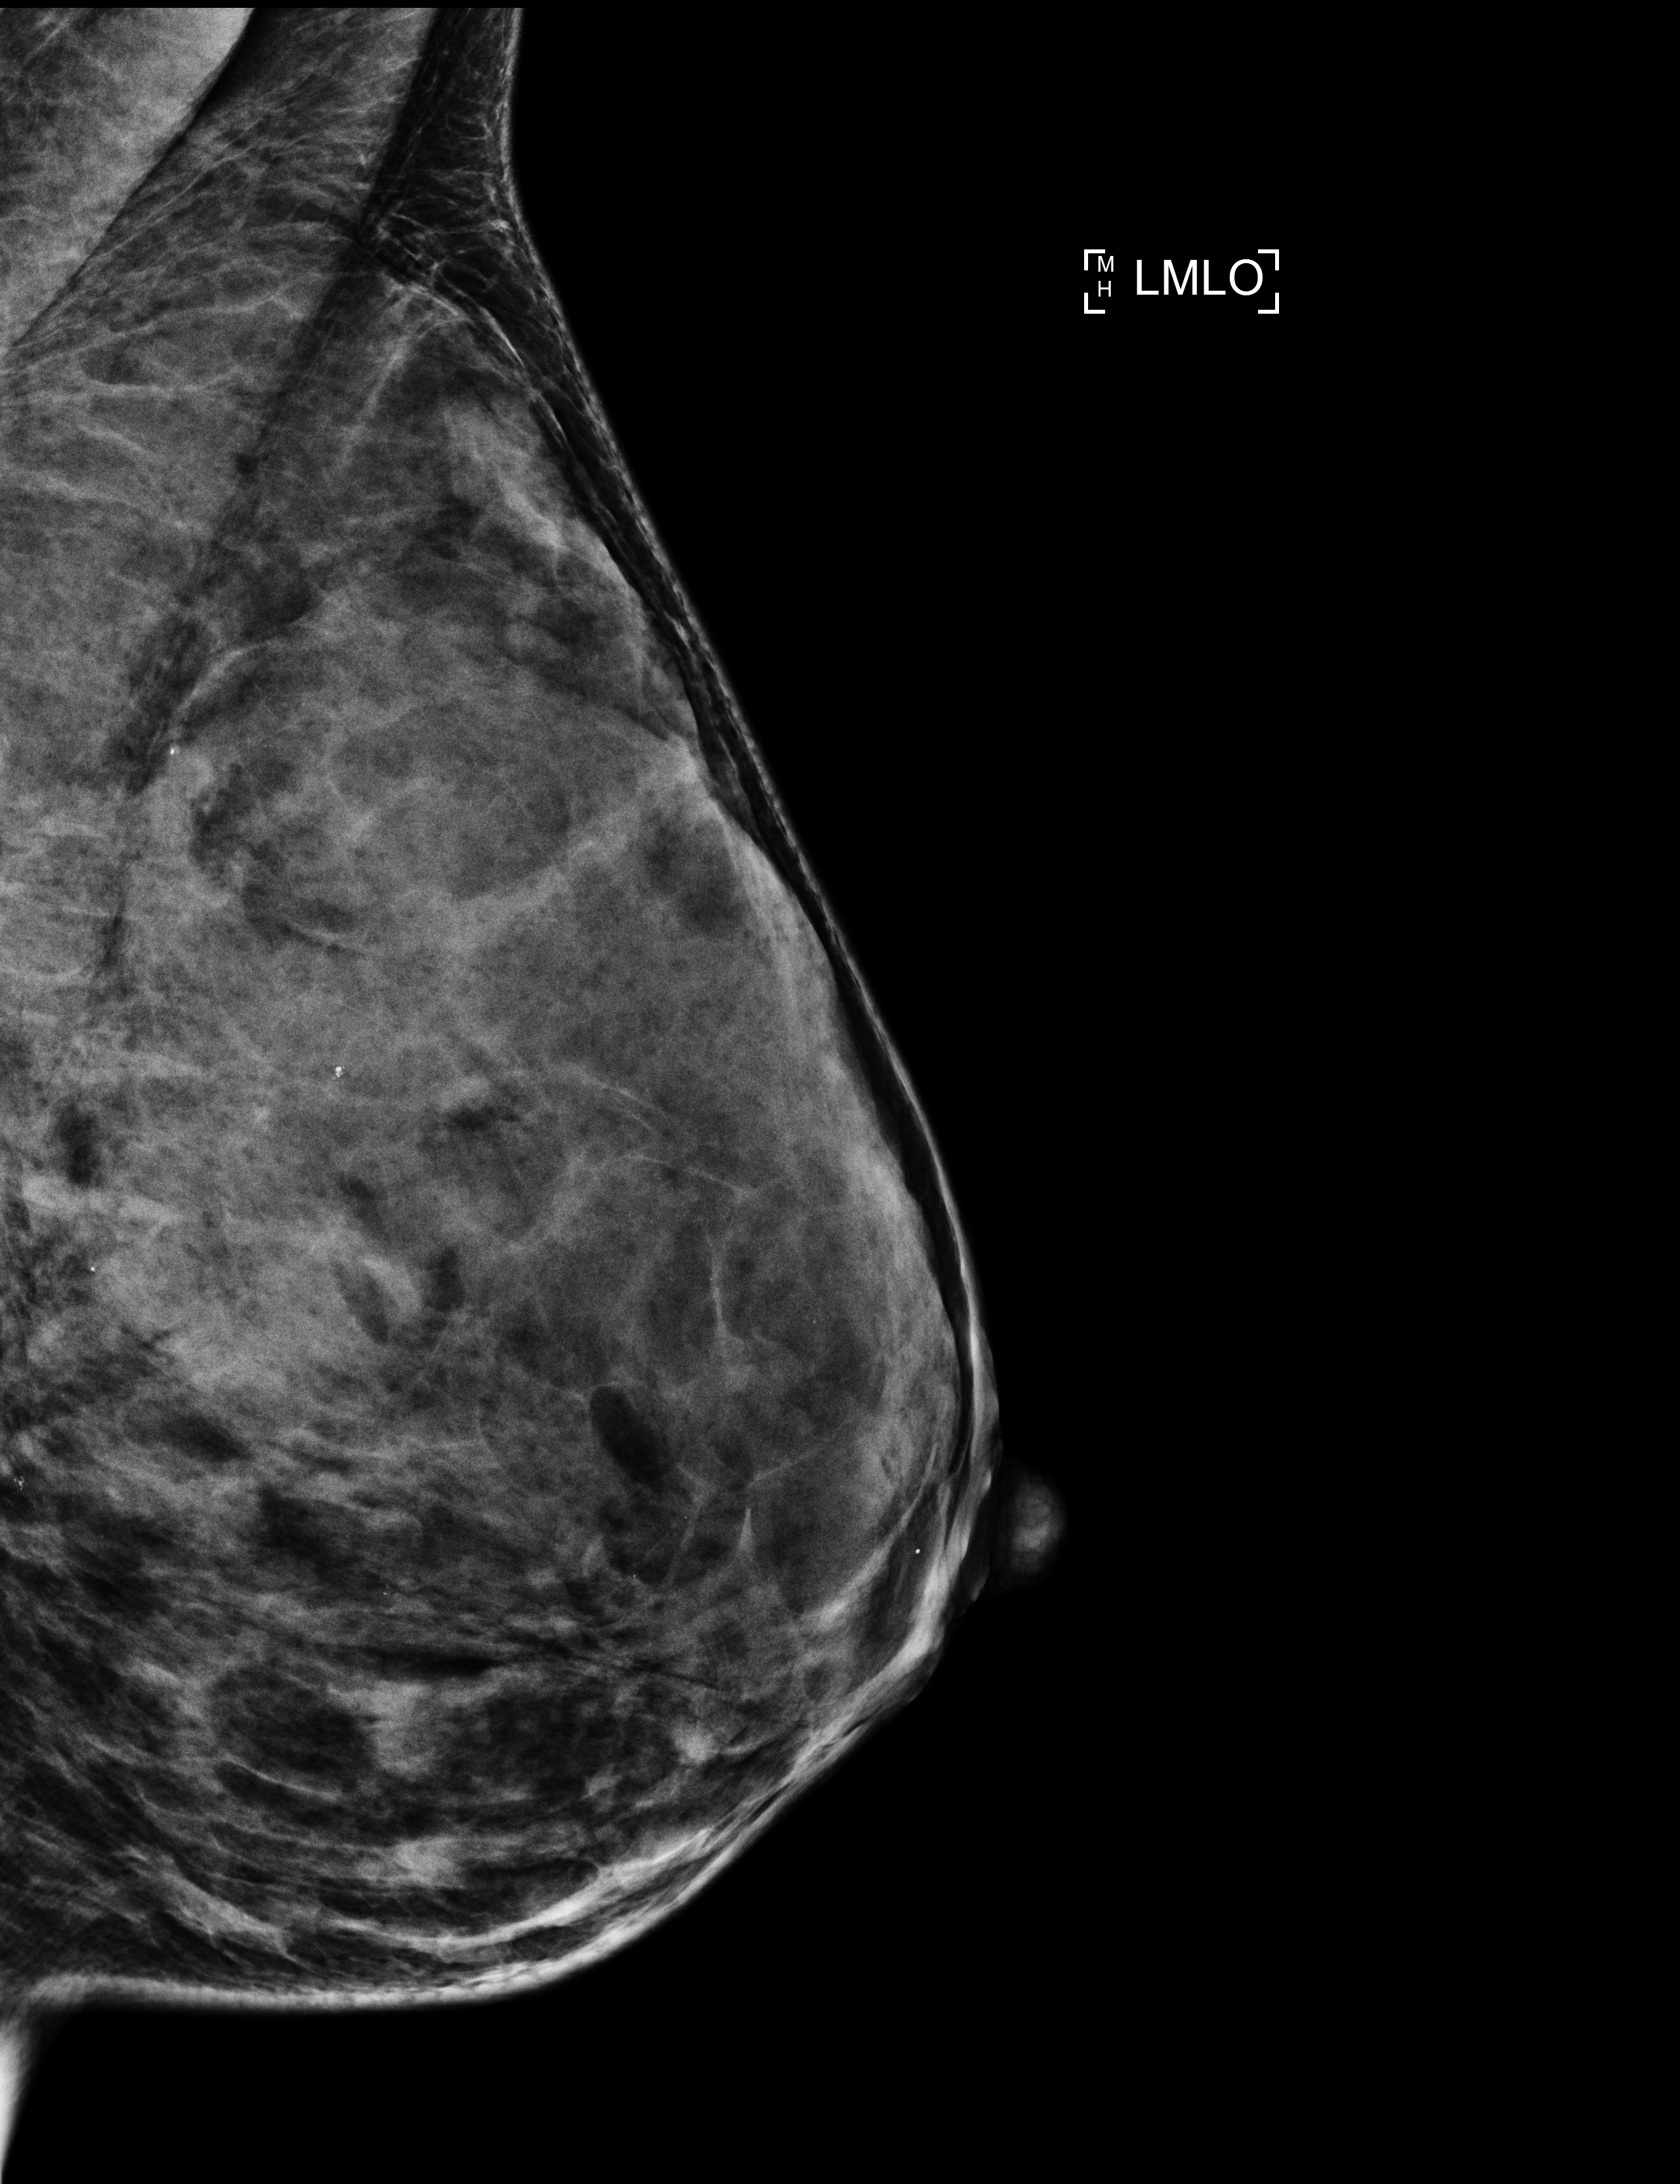
Screening examination; compressed breast thickness 42 mm; system: Selenia Dimensions. Female patient, age 42 years.
Image type: full-field digital mammogram. Breast: left. Projection: MLO view.